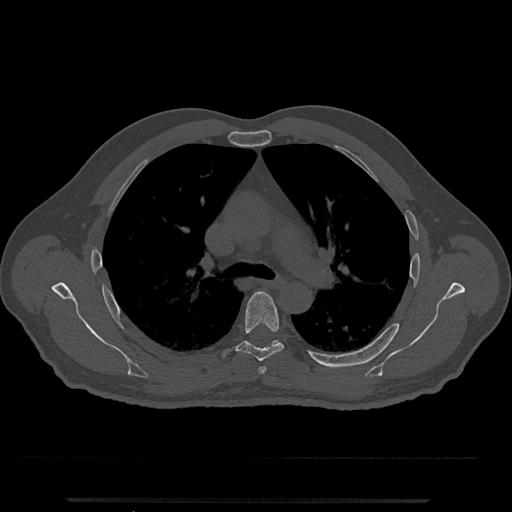
CT including the spine, one axial slice; slice 790 of 797 in the series (ordered by position); reconstruction kernel Br40s/3; 120 kVp; bone window (W 1800 / L 400 HU); 0.5 mm slice thickness; 512 × 512 image matrix, field of view 419 × 419 mm. Male patient, age 63 years. From the clinical record (not read from this slice): primary cancer: prostate.
Outlined on this slice (semi-automatically segmented with operator editing):
- T5 vertebra: bounding box [x1, y1, x2, y2] px = [222, 291, 284, 361]
- T6 vertebra: [271, 340, 280, 346]